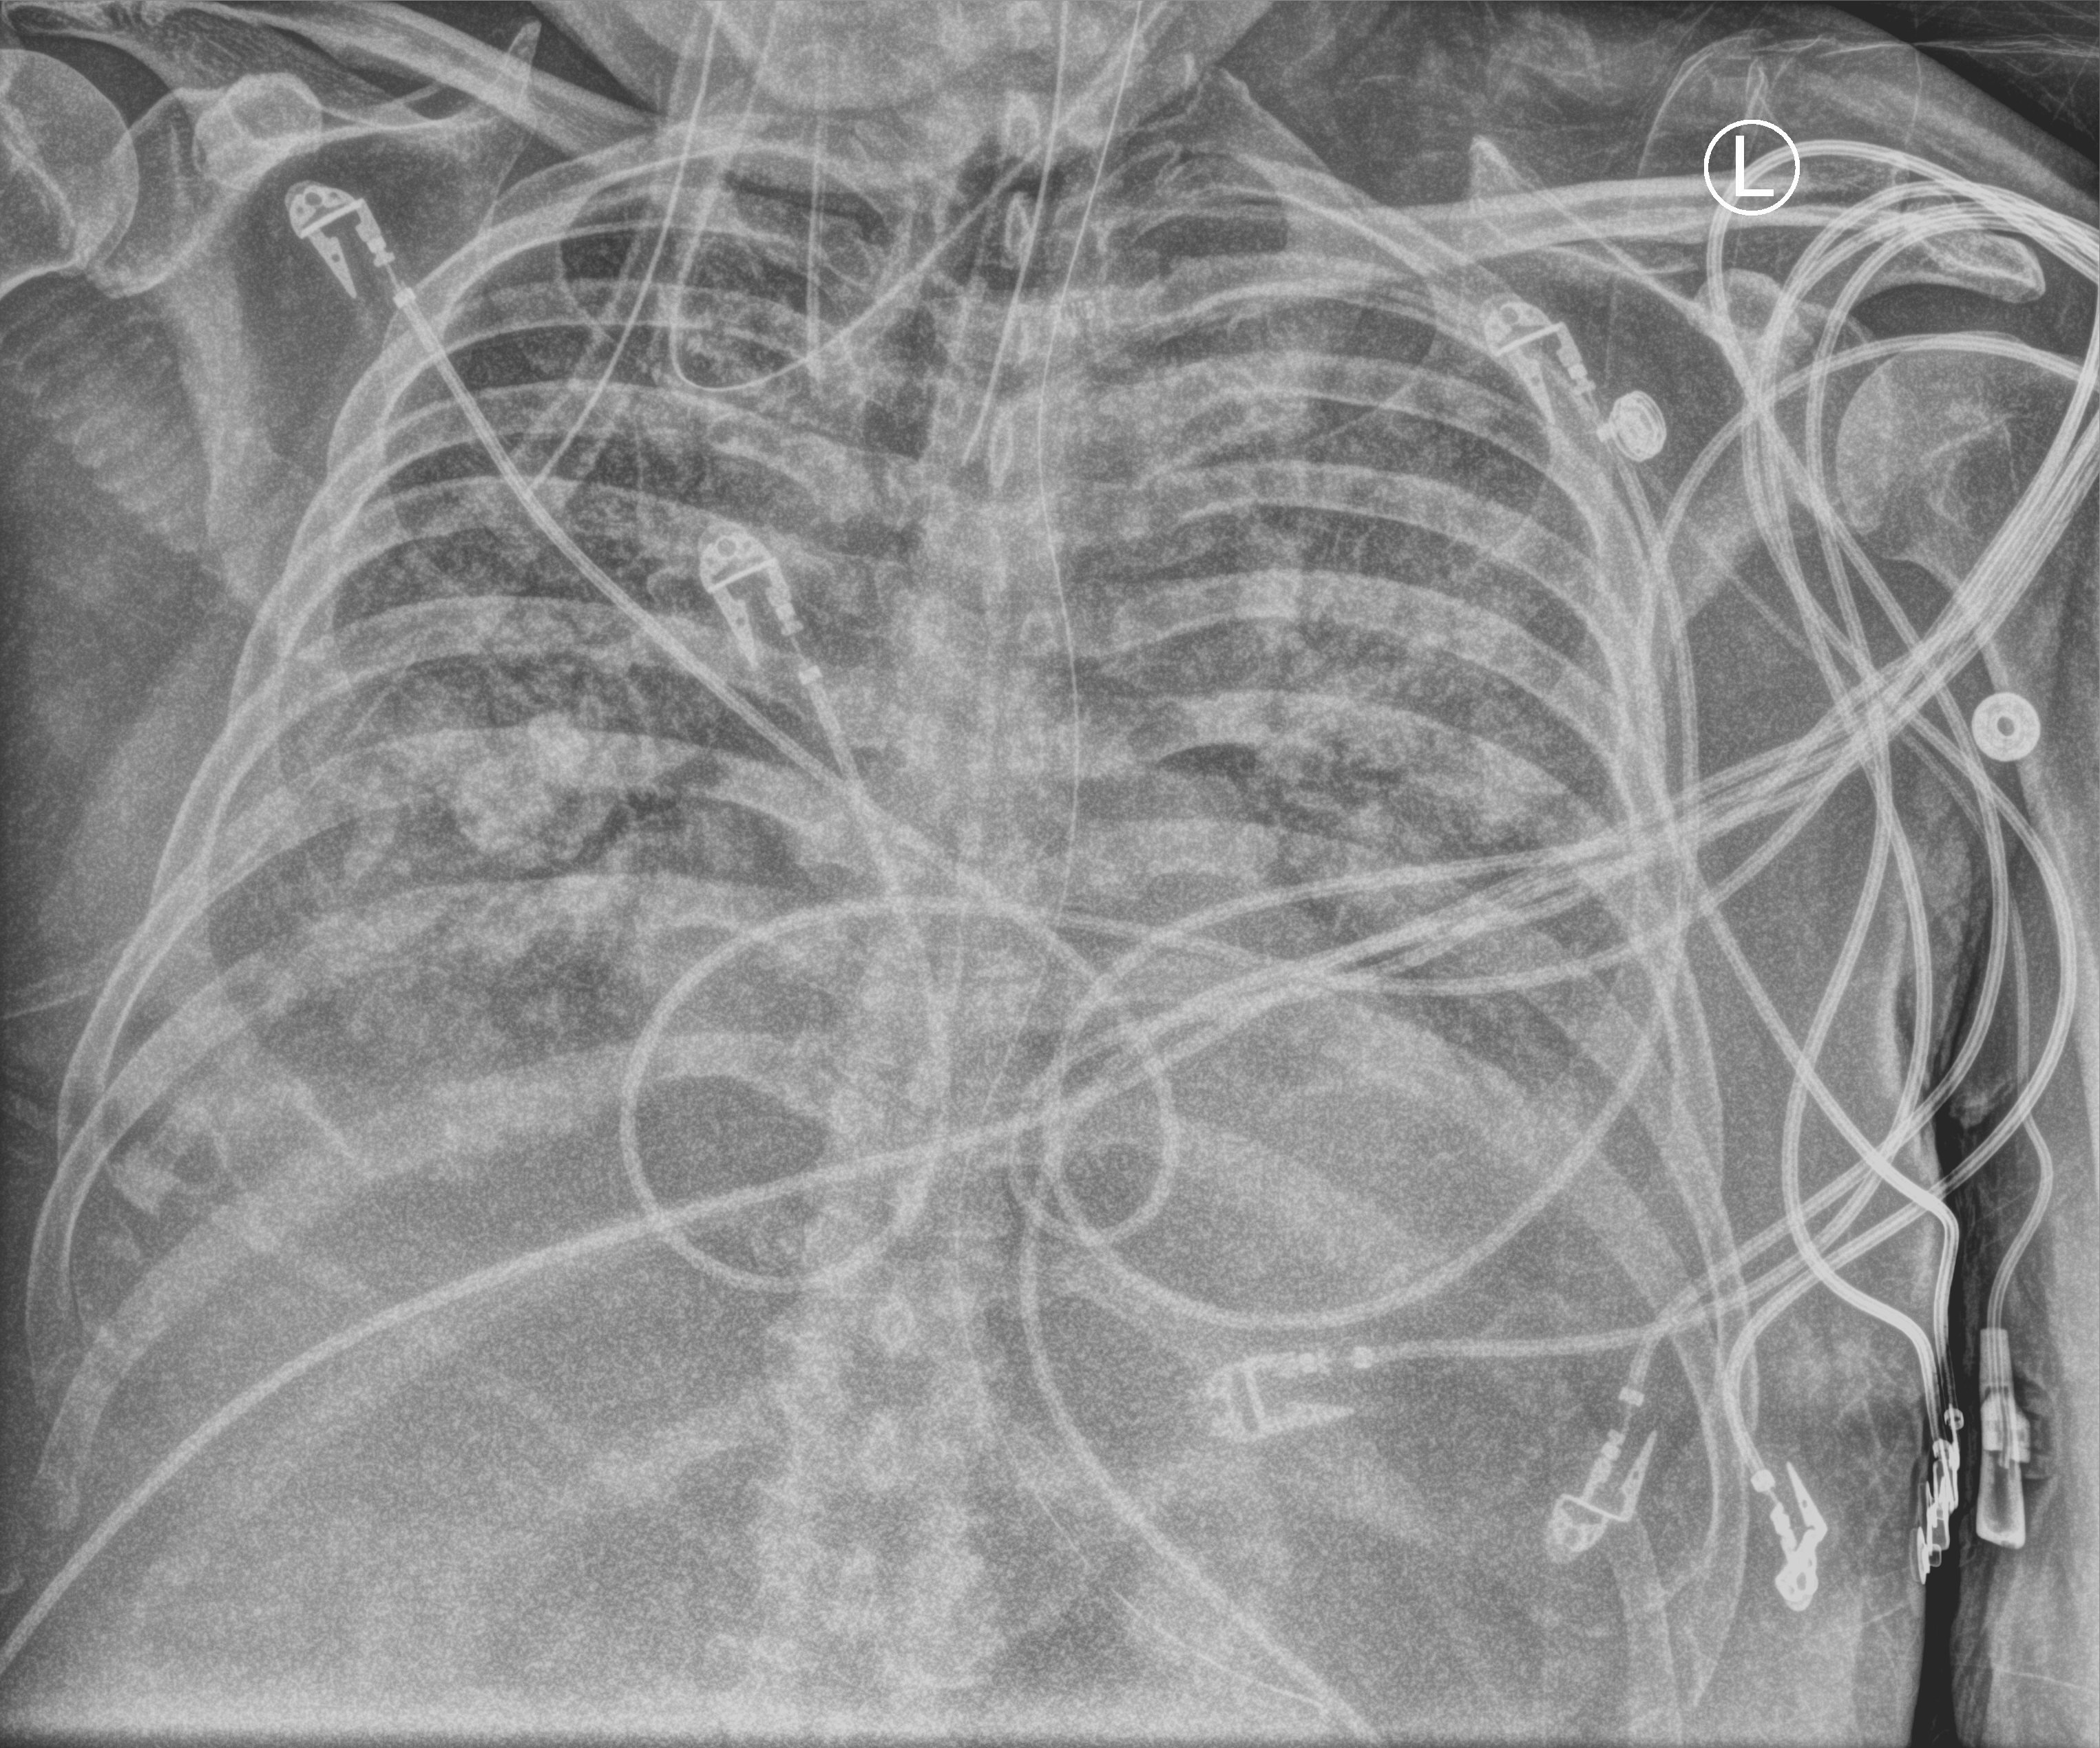
Portable chest radiograph; anteroposterior (AP) projection. Patient hospitalised with COVID-19; male, aged 60–74 years.
Hospital-stay facts (about this admission, not read from this image; timing relative to this image not recorded): admitted to intensive care during this hospital stay: yes; smoking status (admission record): never; mechanically ventilated during this hospital stay: yes.